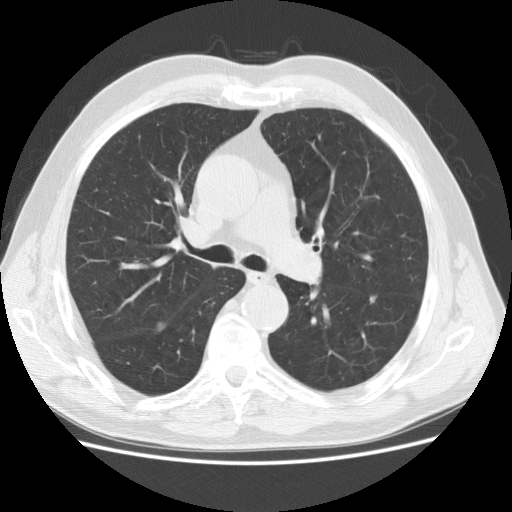
Axial slice from a low-dose chest CT screening exam; baseline screening round; lung window (W 1500 / L -600 HU); 120 kVp; 512 × 512 image matrix. Male participant, aged 73 years at enrolment. Current smoker at enrolment.
Expert reader's lesion annotation, bounding box [x1, y1, x2, y2] px = [349, 285, 397, 318]. Screening reader's record for this exam: no non-calcified nodule ≥4 mm recorded. Official screen result: negative screen, significant abnormalities not suspicious for lung cancer. Participant outcome: lung cancer diagnosed 536 days after this screen (after the second annual screen) — adenocarcinoma, NOS, left lower lobe, poorly differentiated (G3), stage IIA (AJCC 6th edition), 12 mm at pathology.